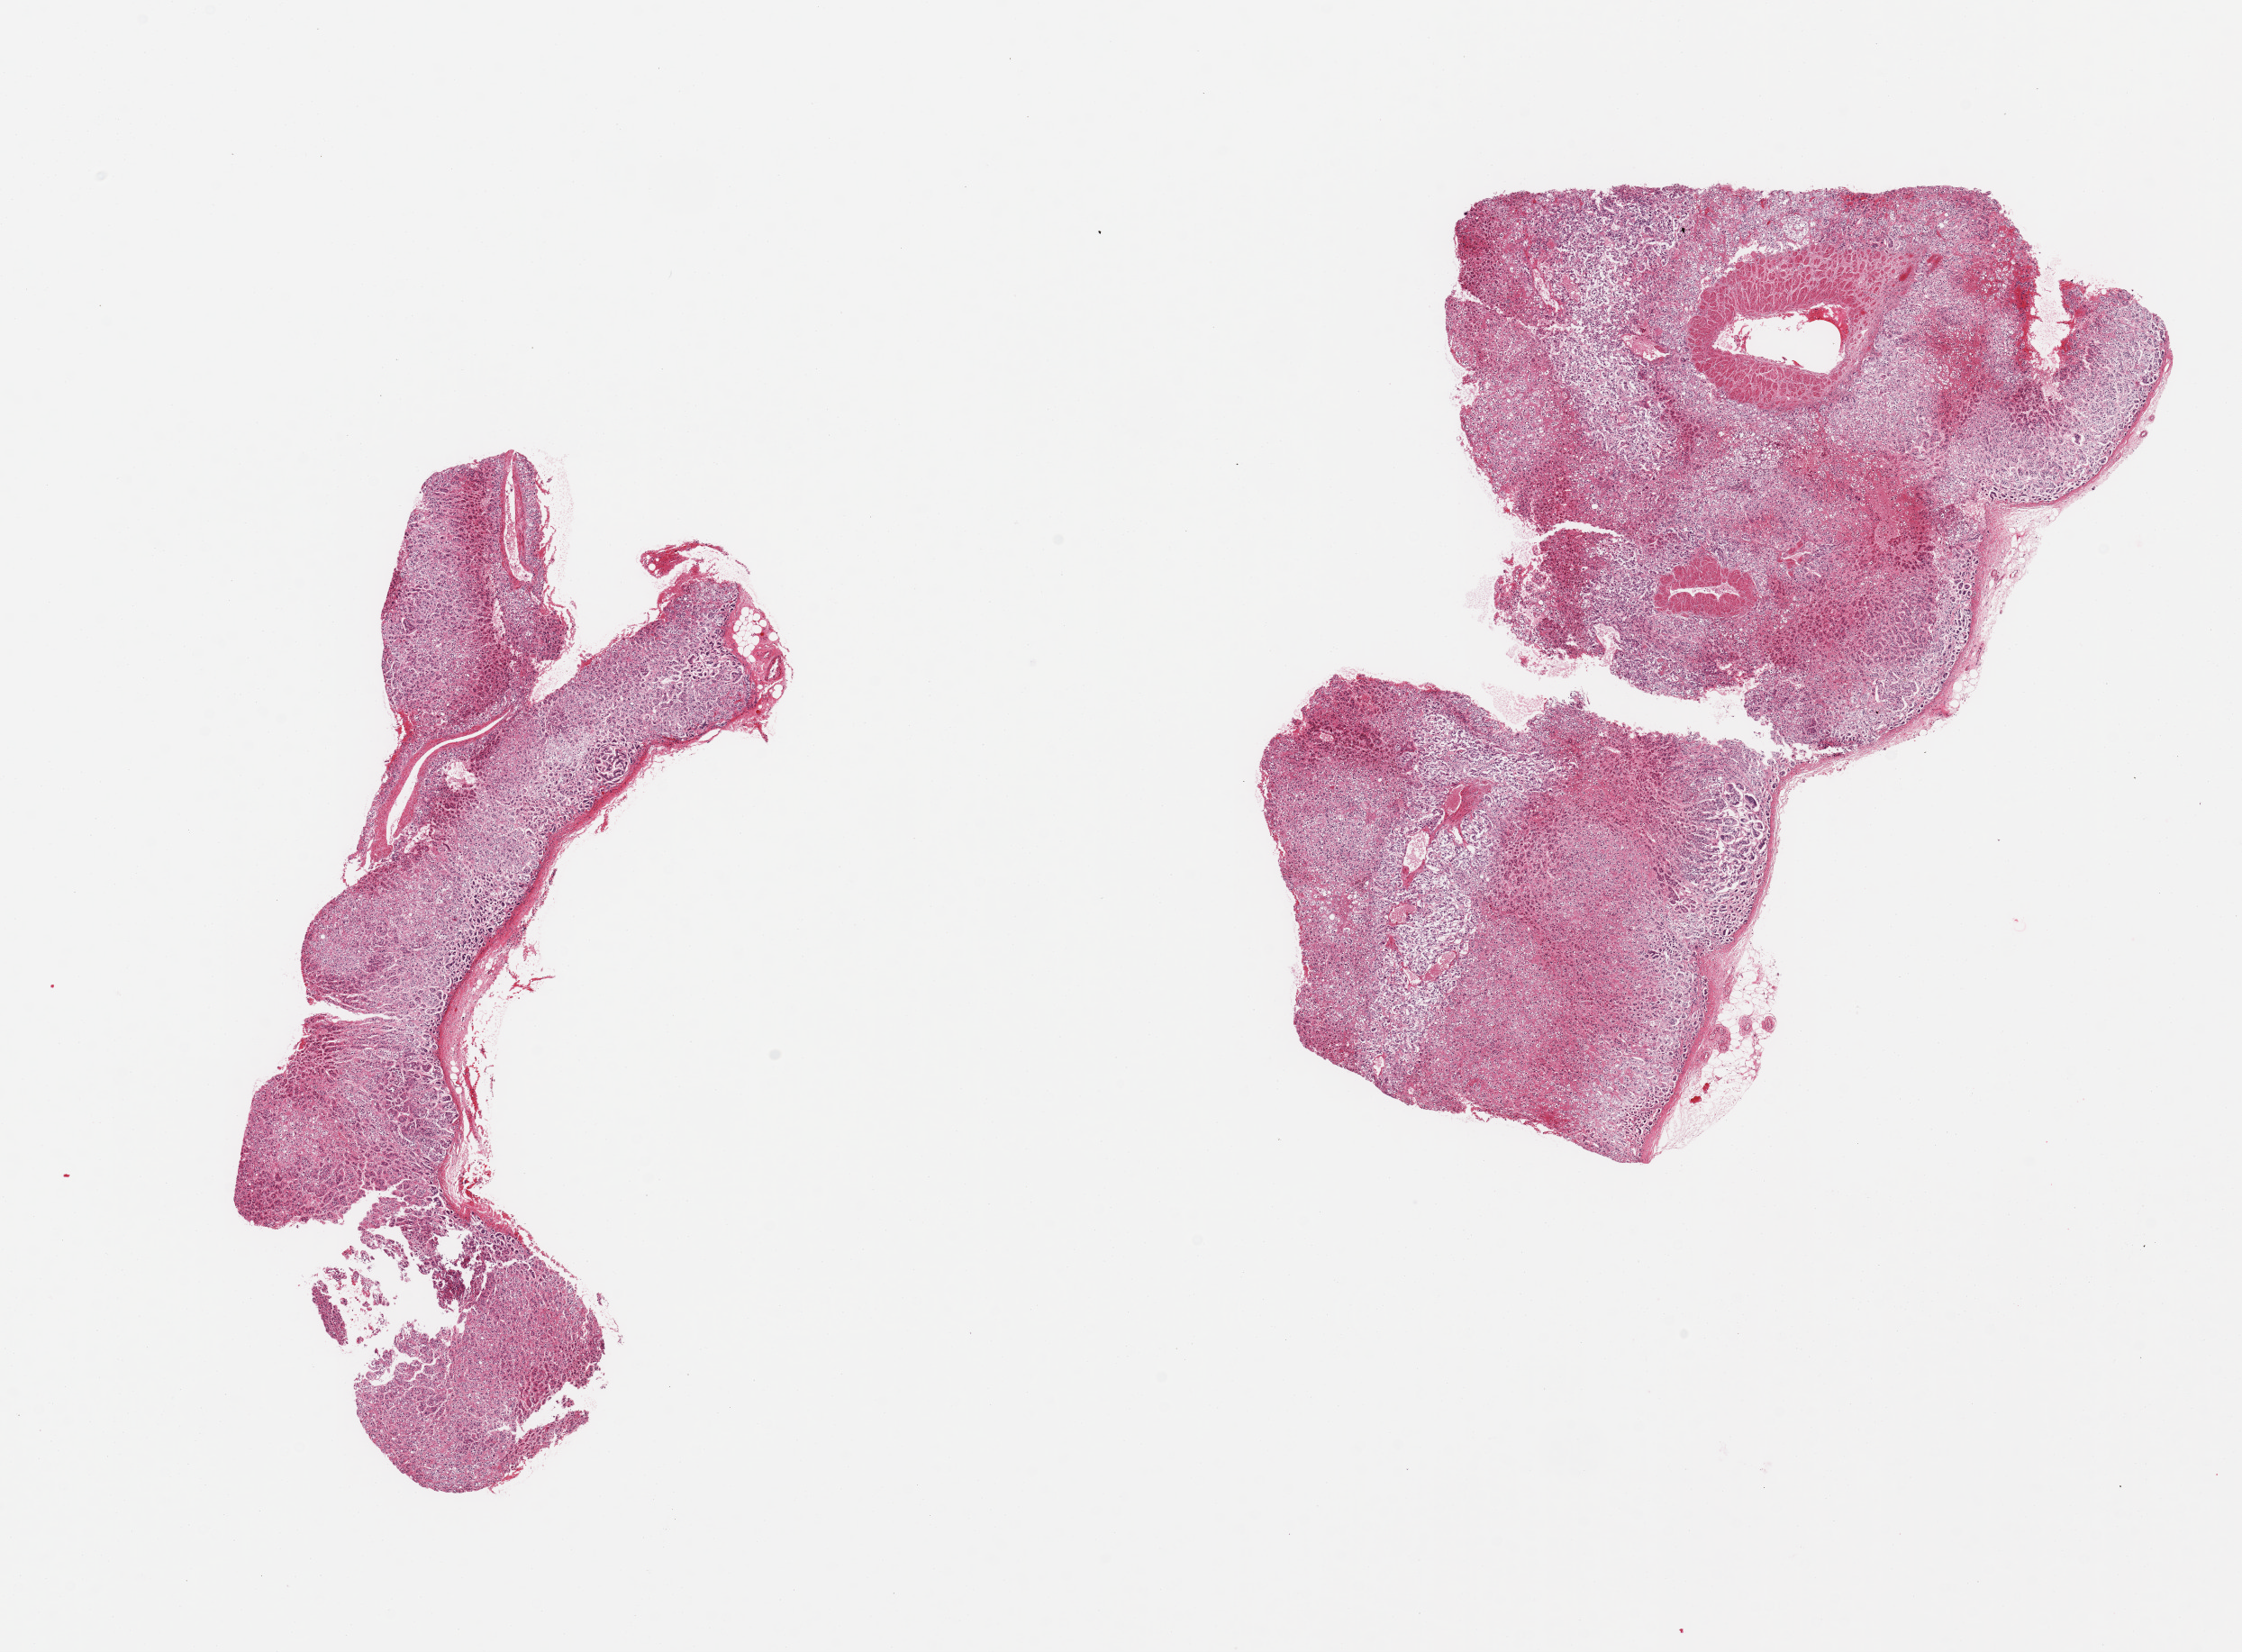
Whole-slide image, haematoxylin and eosin stain — a low-resolution overview of the entire scanned area, about 19.7 x 14.5 mm, PAXgene-fixed paraffin-embedded (PFPE) section, section of adrenal gland (target tissue), donor tissue sample. Donor: female.
* reviewer comment on this tissue sample: 2 pieces; well trimmed